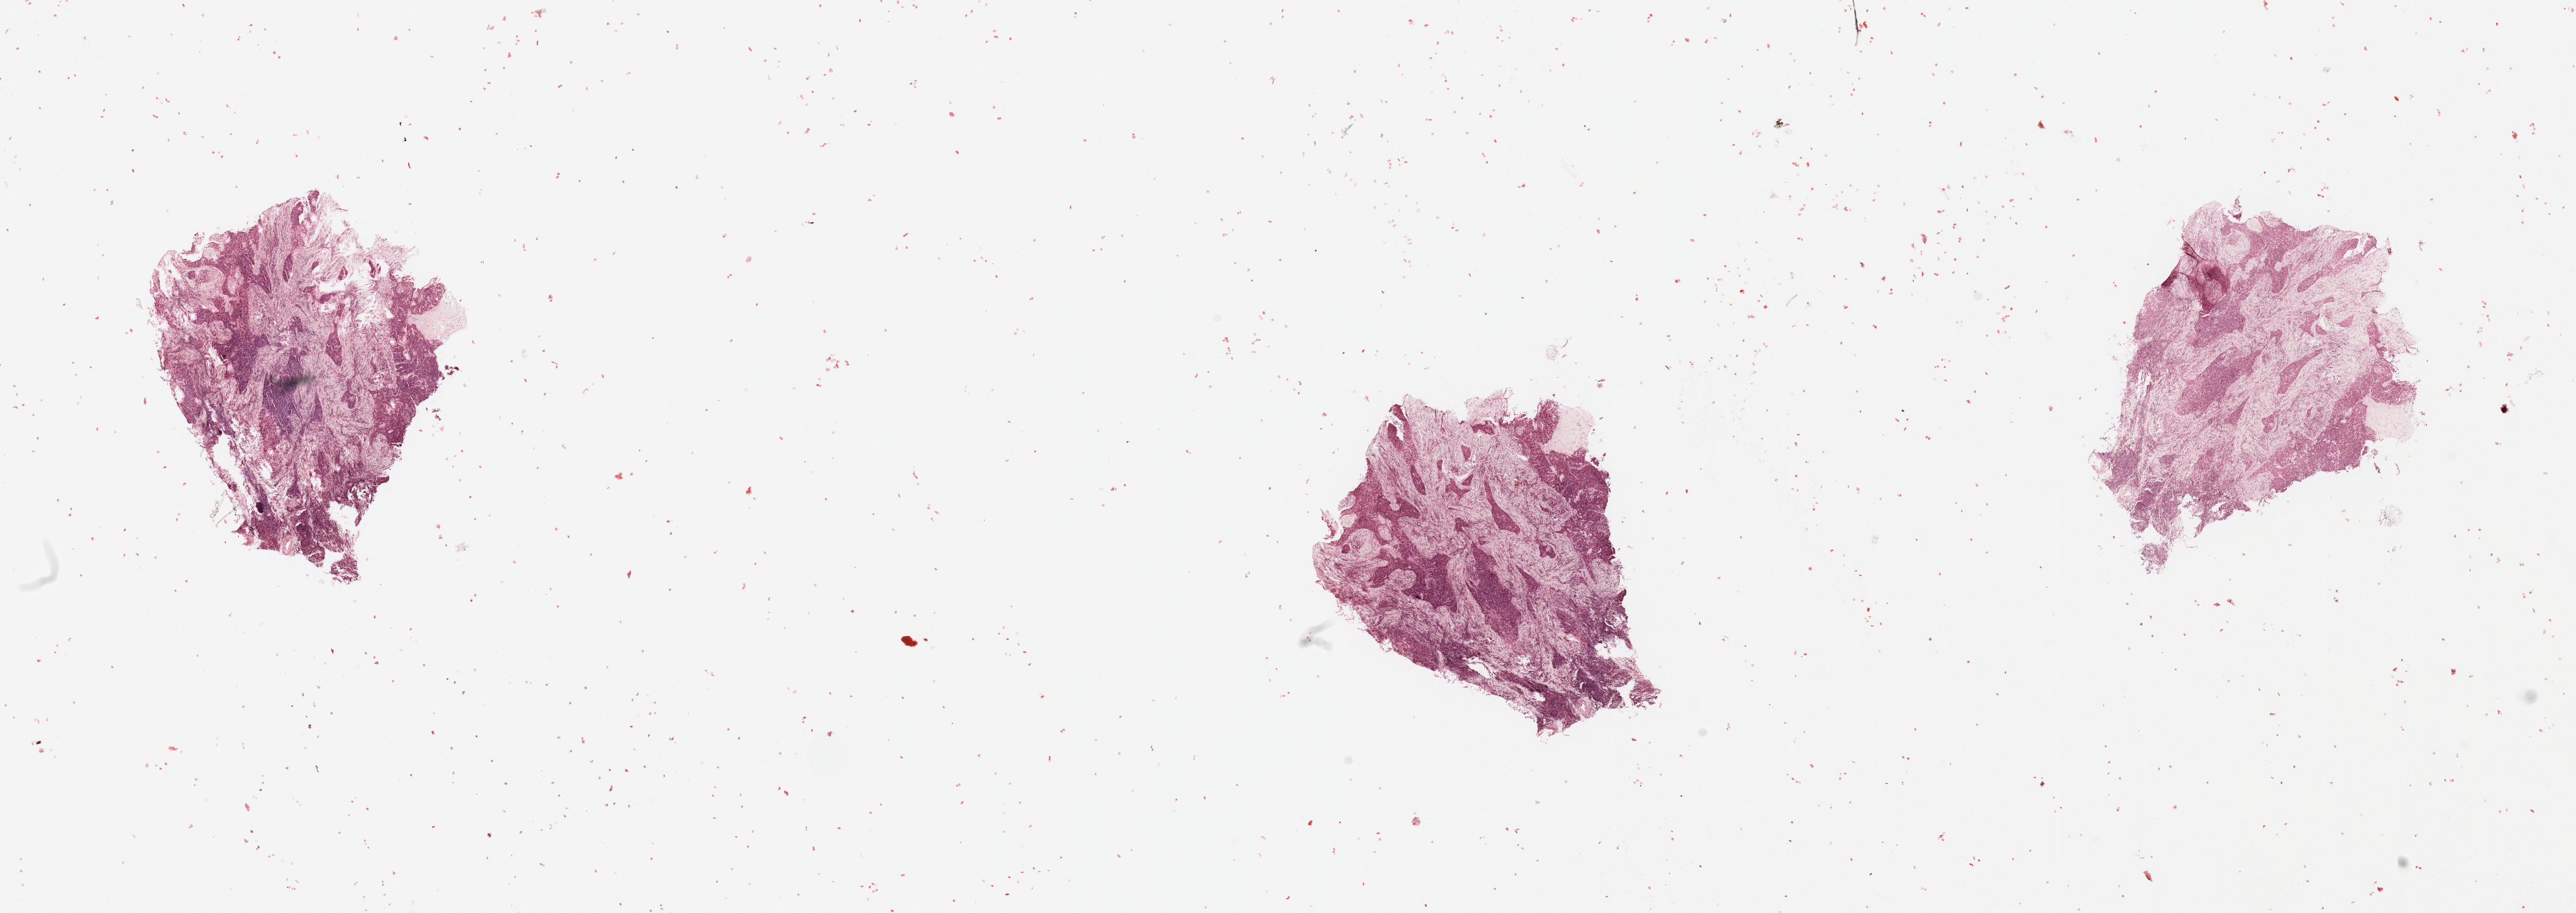
Digitized H&E-stained tissue section (whole slide), whole scanned area (about 28.5 x 10.1 mm) shown as a low-resolution overview; head and neck, tissue type not recorded. Patient: male, age 68 years.
* patient diagnosis: Squamous cell carcinoma, NOS (larynx, NOS)